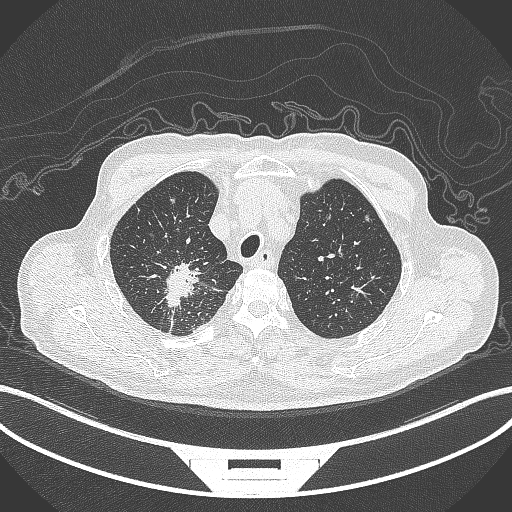
Chest CT, one axial slice. Position 308 of 407 along the scan axis. Reconstruction kernel B70f. 120 kVp. Lung window (W 1500 / L -600 HU). 1 mm slice thickness. 512 × 512 image matrix, field of view 400 × 400 mm. Male patient, age 69 years. Case-level facts recorded for this patient, not image findings: clinical TNM (as recorded): T1c N1 M1.
Outlined on this slice (rectangle marked by the reading radiologist):
- lung tumour (recorded histology: adenocarcinoma): bounding box [x1, y1, x2, y2] px = [163, 260, 209, 318]